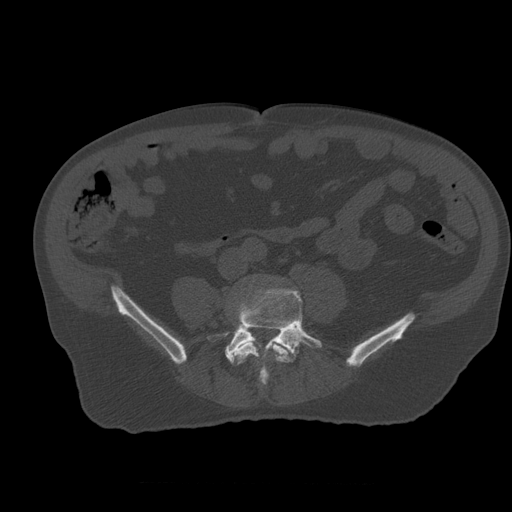
CT including the spine, one axial slice. Reconstruction kernel STANDARD. Bone window (W 1800 / L 400 HU). 1.25 mm slice thickness. 512 × 512 image matrix. Patient age 73 years. Case-level facts recorded for this patient, not image findings: primary cancer: prostate.
Annotated regions visible in this slice (semi-automatically segmented with operator editing):
- L4 vertebra: bounding box (x1, y1, x2, y2) in pixels: (235, 341, 291, 385)
- L5 vertebra: (218, 290, 322, 385)